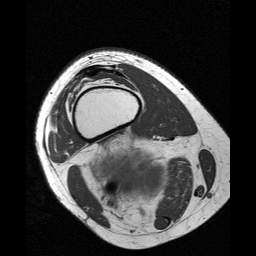
MRI of an extremity soft-tissue mass, one axial slice; position 23 of 25 along the scan axis; 256 × 256 image matrix, field of view 160 × 160 mm. Female patient. Case-level facts recorded for this patient, not image findings: histological type: liposarcoma; site of the primary tumour: right thigh.
Annotated regions visible in this slice (manually delineated by an expert):
- gross tumour volume (mass): box from (x=88, y=145) to (x=171, y=205) px